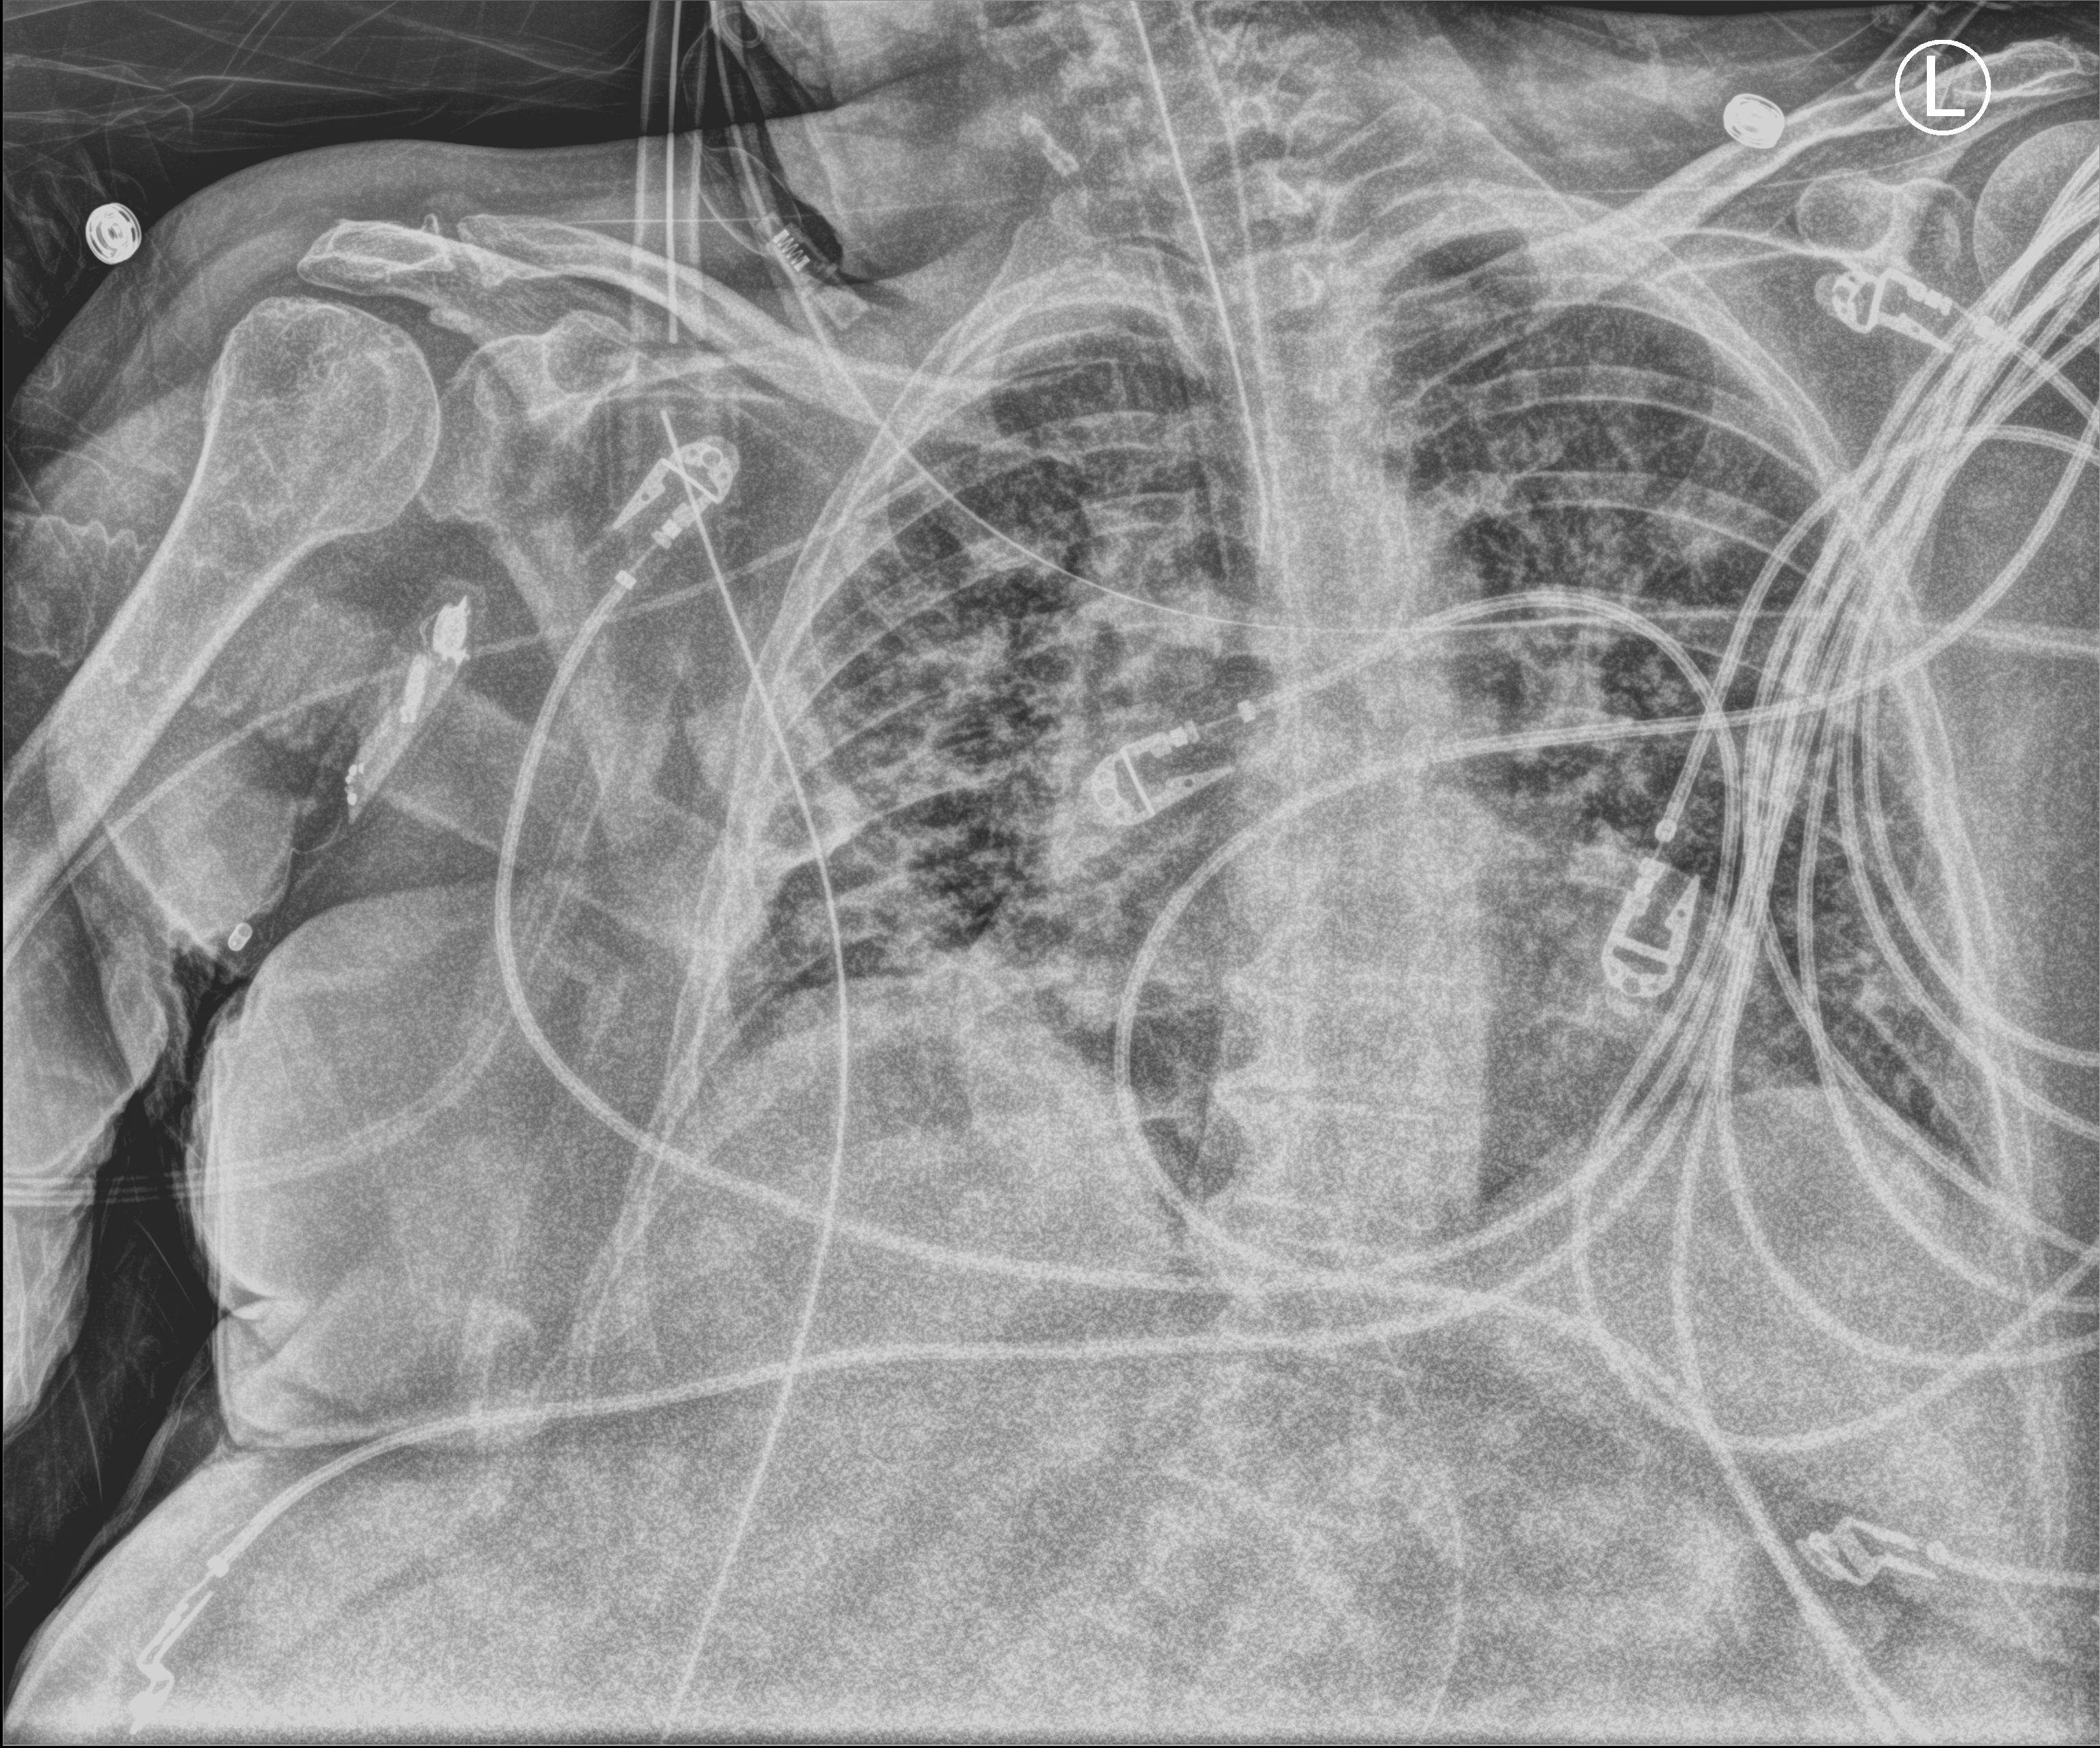
Bedside chest radiograph (computed radiography); anteroposterior (AP) projection. Patient hospitalised with COVID-19; female, aged 75–90 years.
From the hospital-stay record, not from the radiograph (when in the stay this image was taken is not recorded):
- mechanically ventilated during this hospital stay: yes
- chronic kidney disease (admission record): no